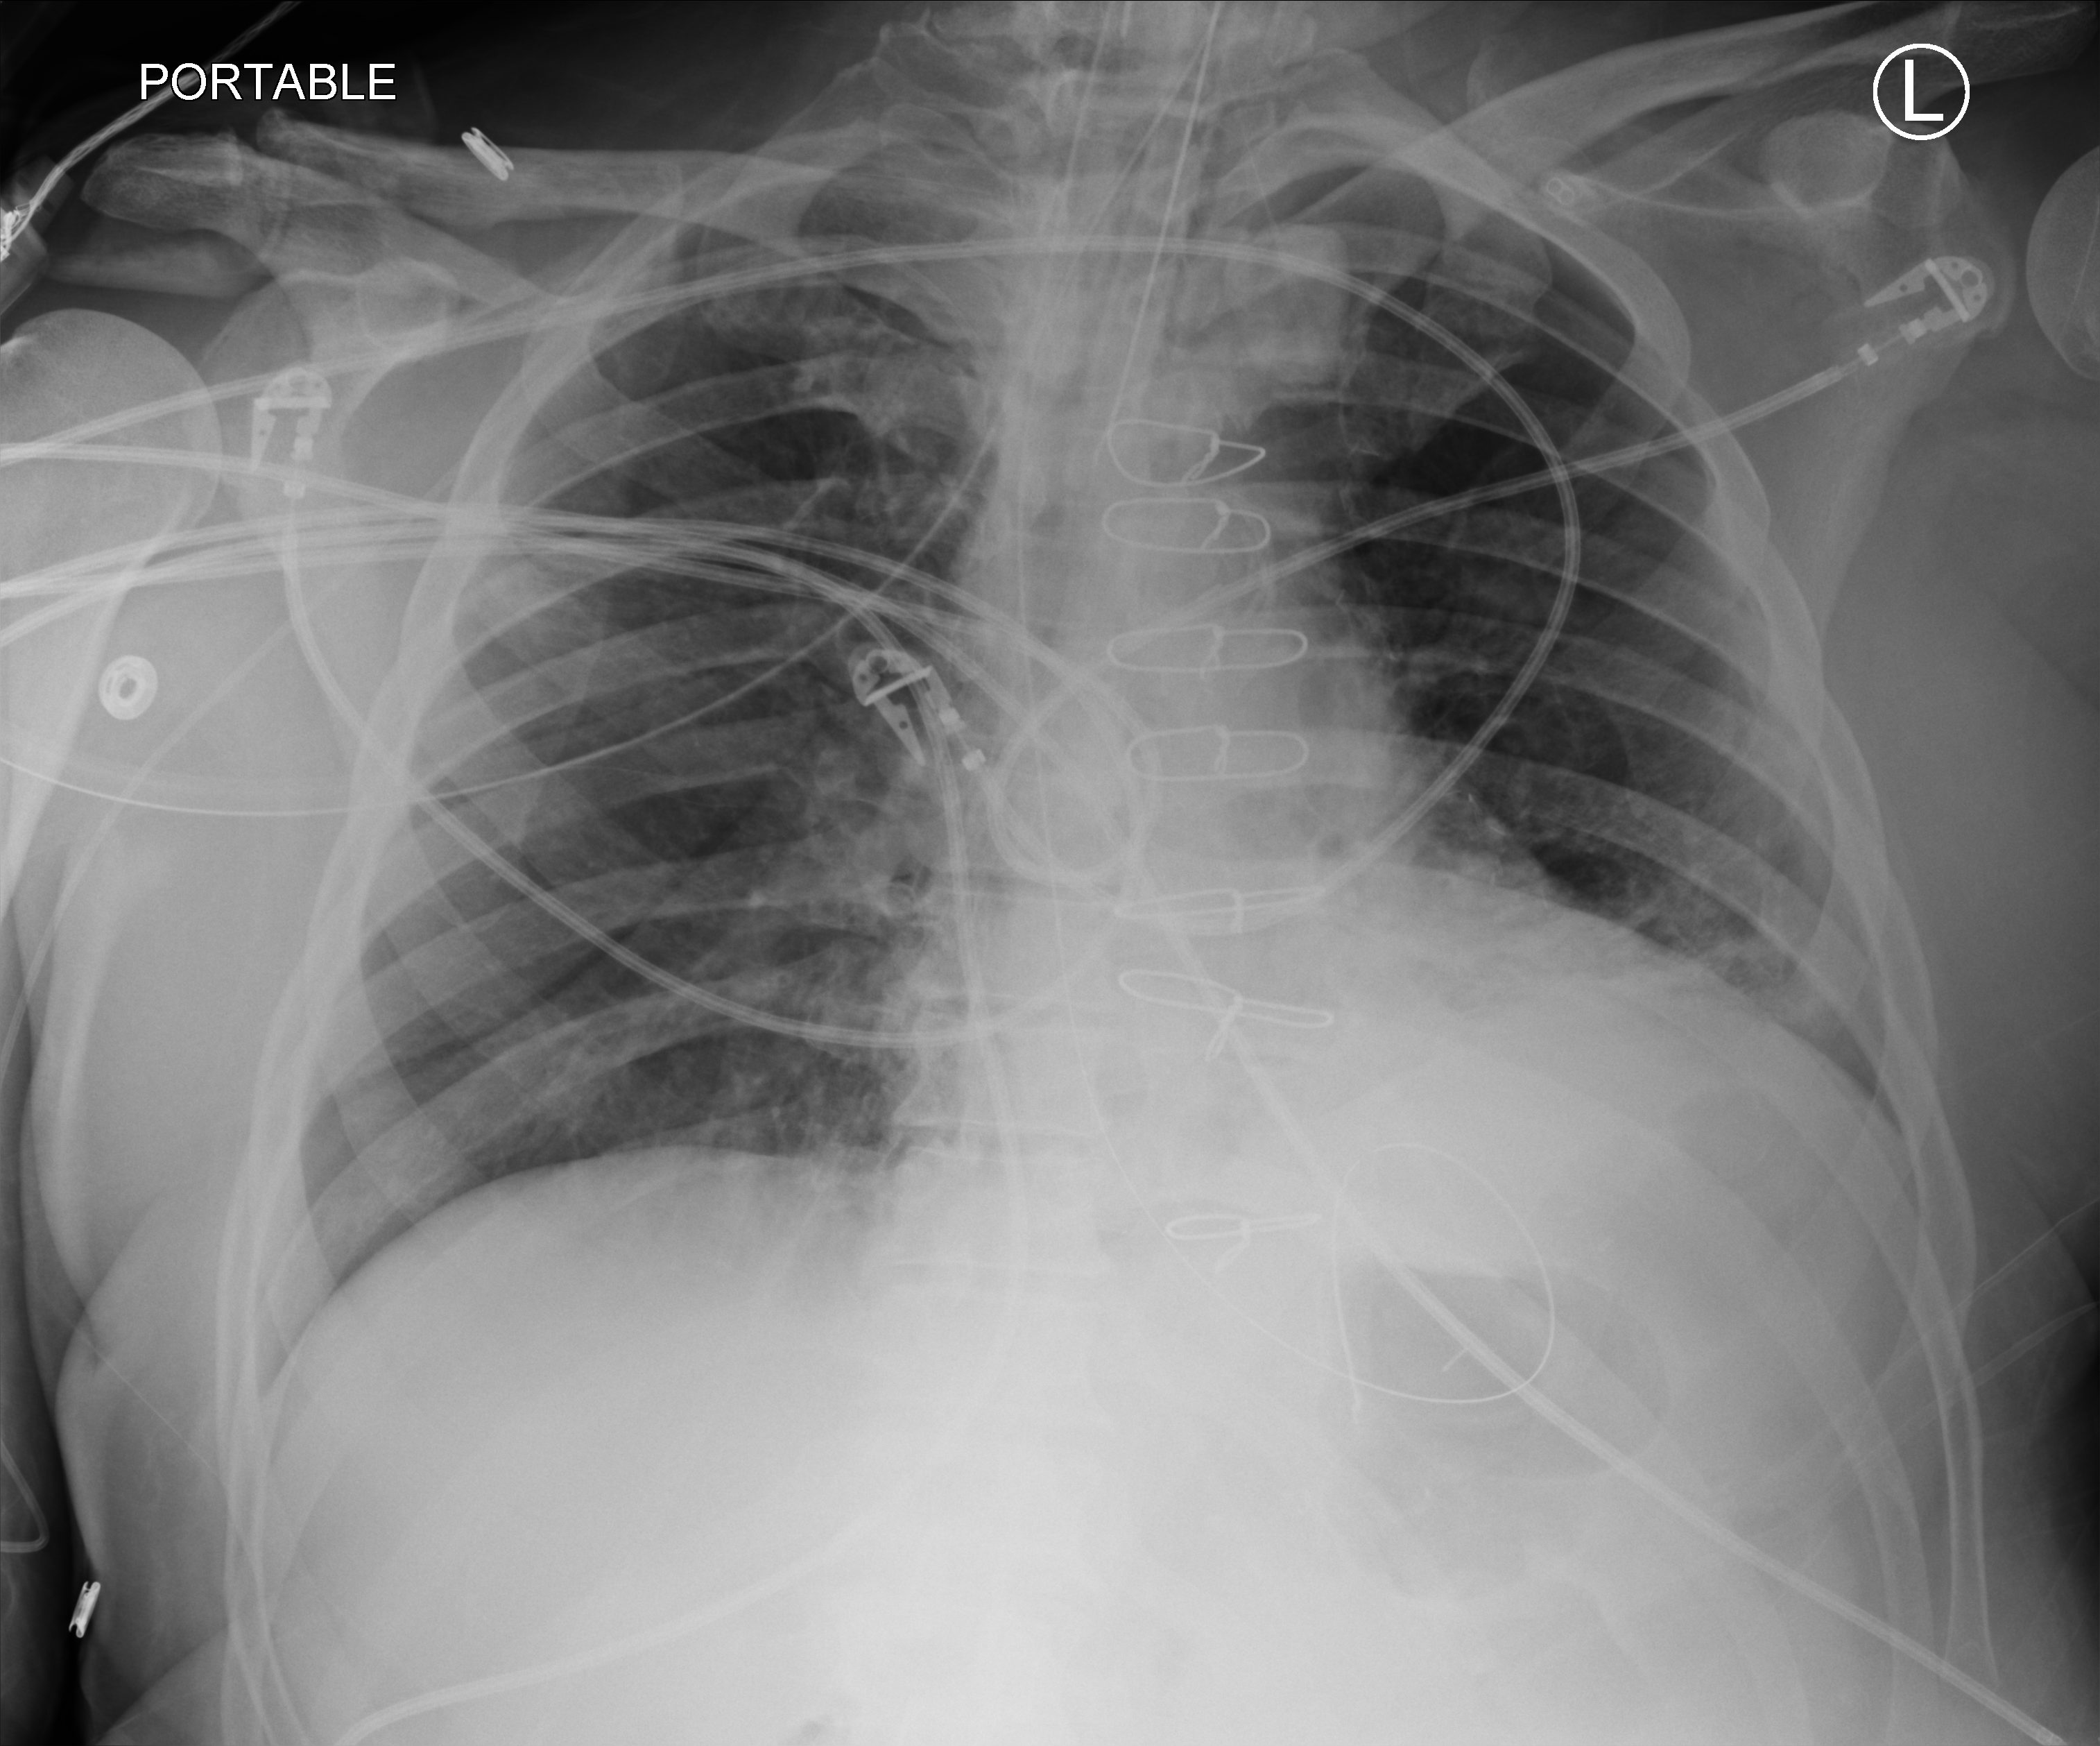
Portable chest radiograph, anteroposterior (AP) projection. Patient hospitalised with COVID-19; male, aged 60–74 years.
Hospital-stay facts (about this admission, not read from this image; timing relative to this image not recorded): chronic kidney disease (admission record): no.